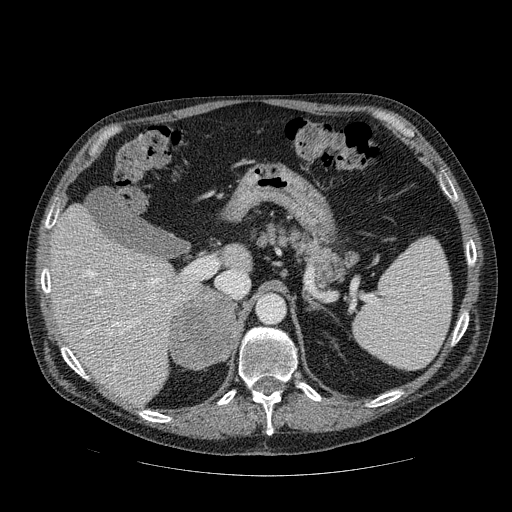
Contrast-enhanced abdominal CT, one axial slice; slice 62 of 111 in the series (ordered by position); 120 kVp; intravenous contrast given; soft-tissue window (W 400 / L 40 HU); 2.5 mm slice thickness; 512 × 512 image matrix. Male patient, age 56 years. Case-level facts recorded for this patient, not image findings: diagnosis: adrenocortical carcinoma; tumour side: right adrenal; tumour size at pathology: 9 cm; Ki-67 index: 48 %; stage (as recorded): 4.
Annotated regions visible in this slice (semi-automatically segmented with operator editing):
- mass: bounding box <171,290,237,368> (left, top, right, bottom; pixels)